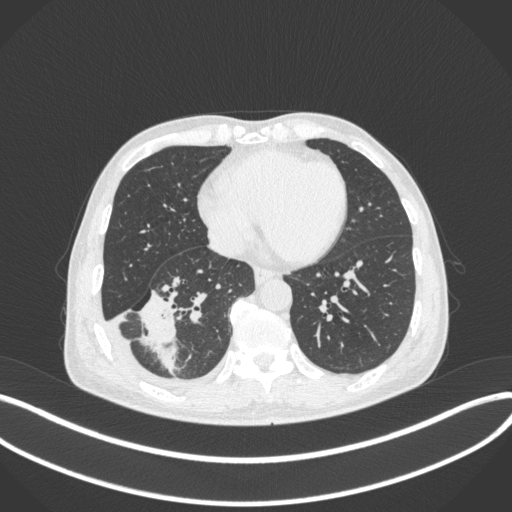
Chest CT, one axial slice. Position 133 of 385 along the scan axis. 120 kVp. Lung window (W 1500 / L -600 HU). 1 mm slice thickness. 512 × 512 image matrix. Male patient, age 64 years. Case-level facts recorded for this patient, not image findings: clinical TNM (as recorded): T3 N0 M0; histopathological grade: G2-3.
Outlined on this slice (bounding box drawn by a radiologist):
- lung tumour (recorded histology: adenocarcinoma): bounding box [x1, y1, x2, y2] px = [133, 285, 183, 378]